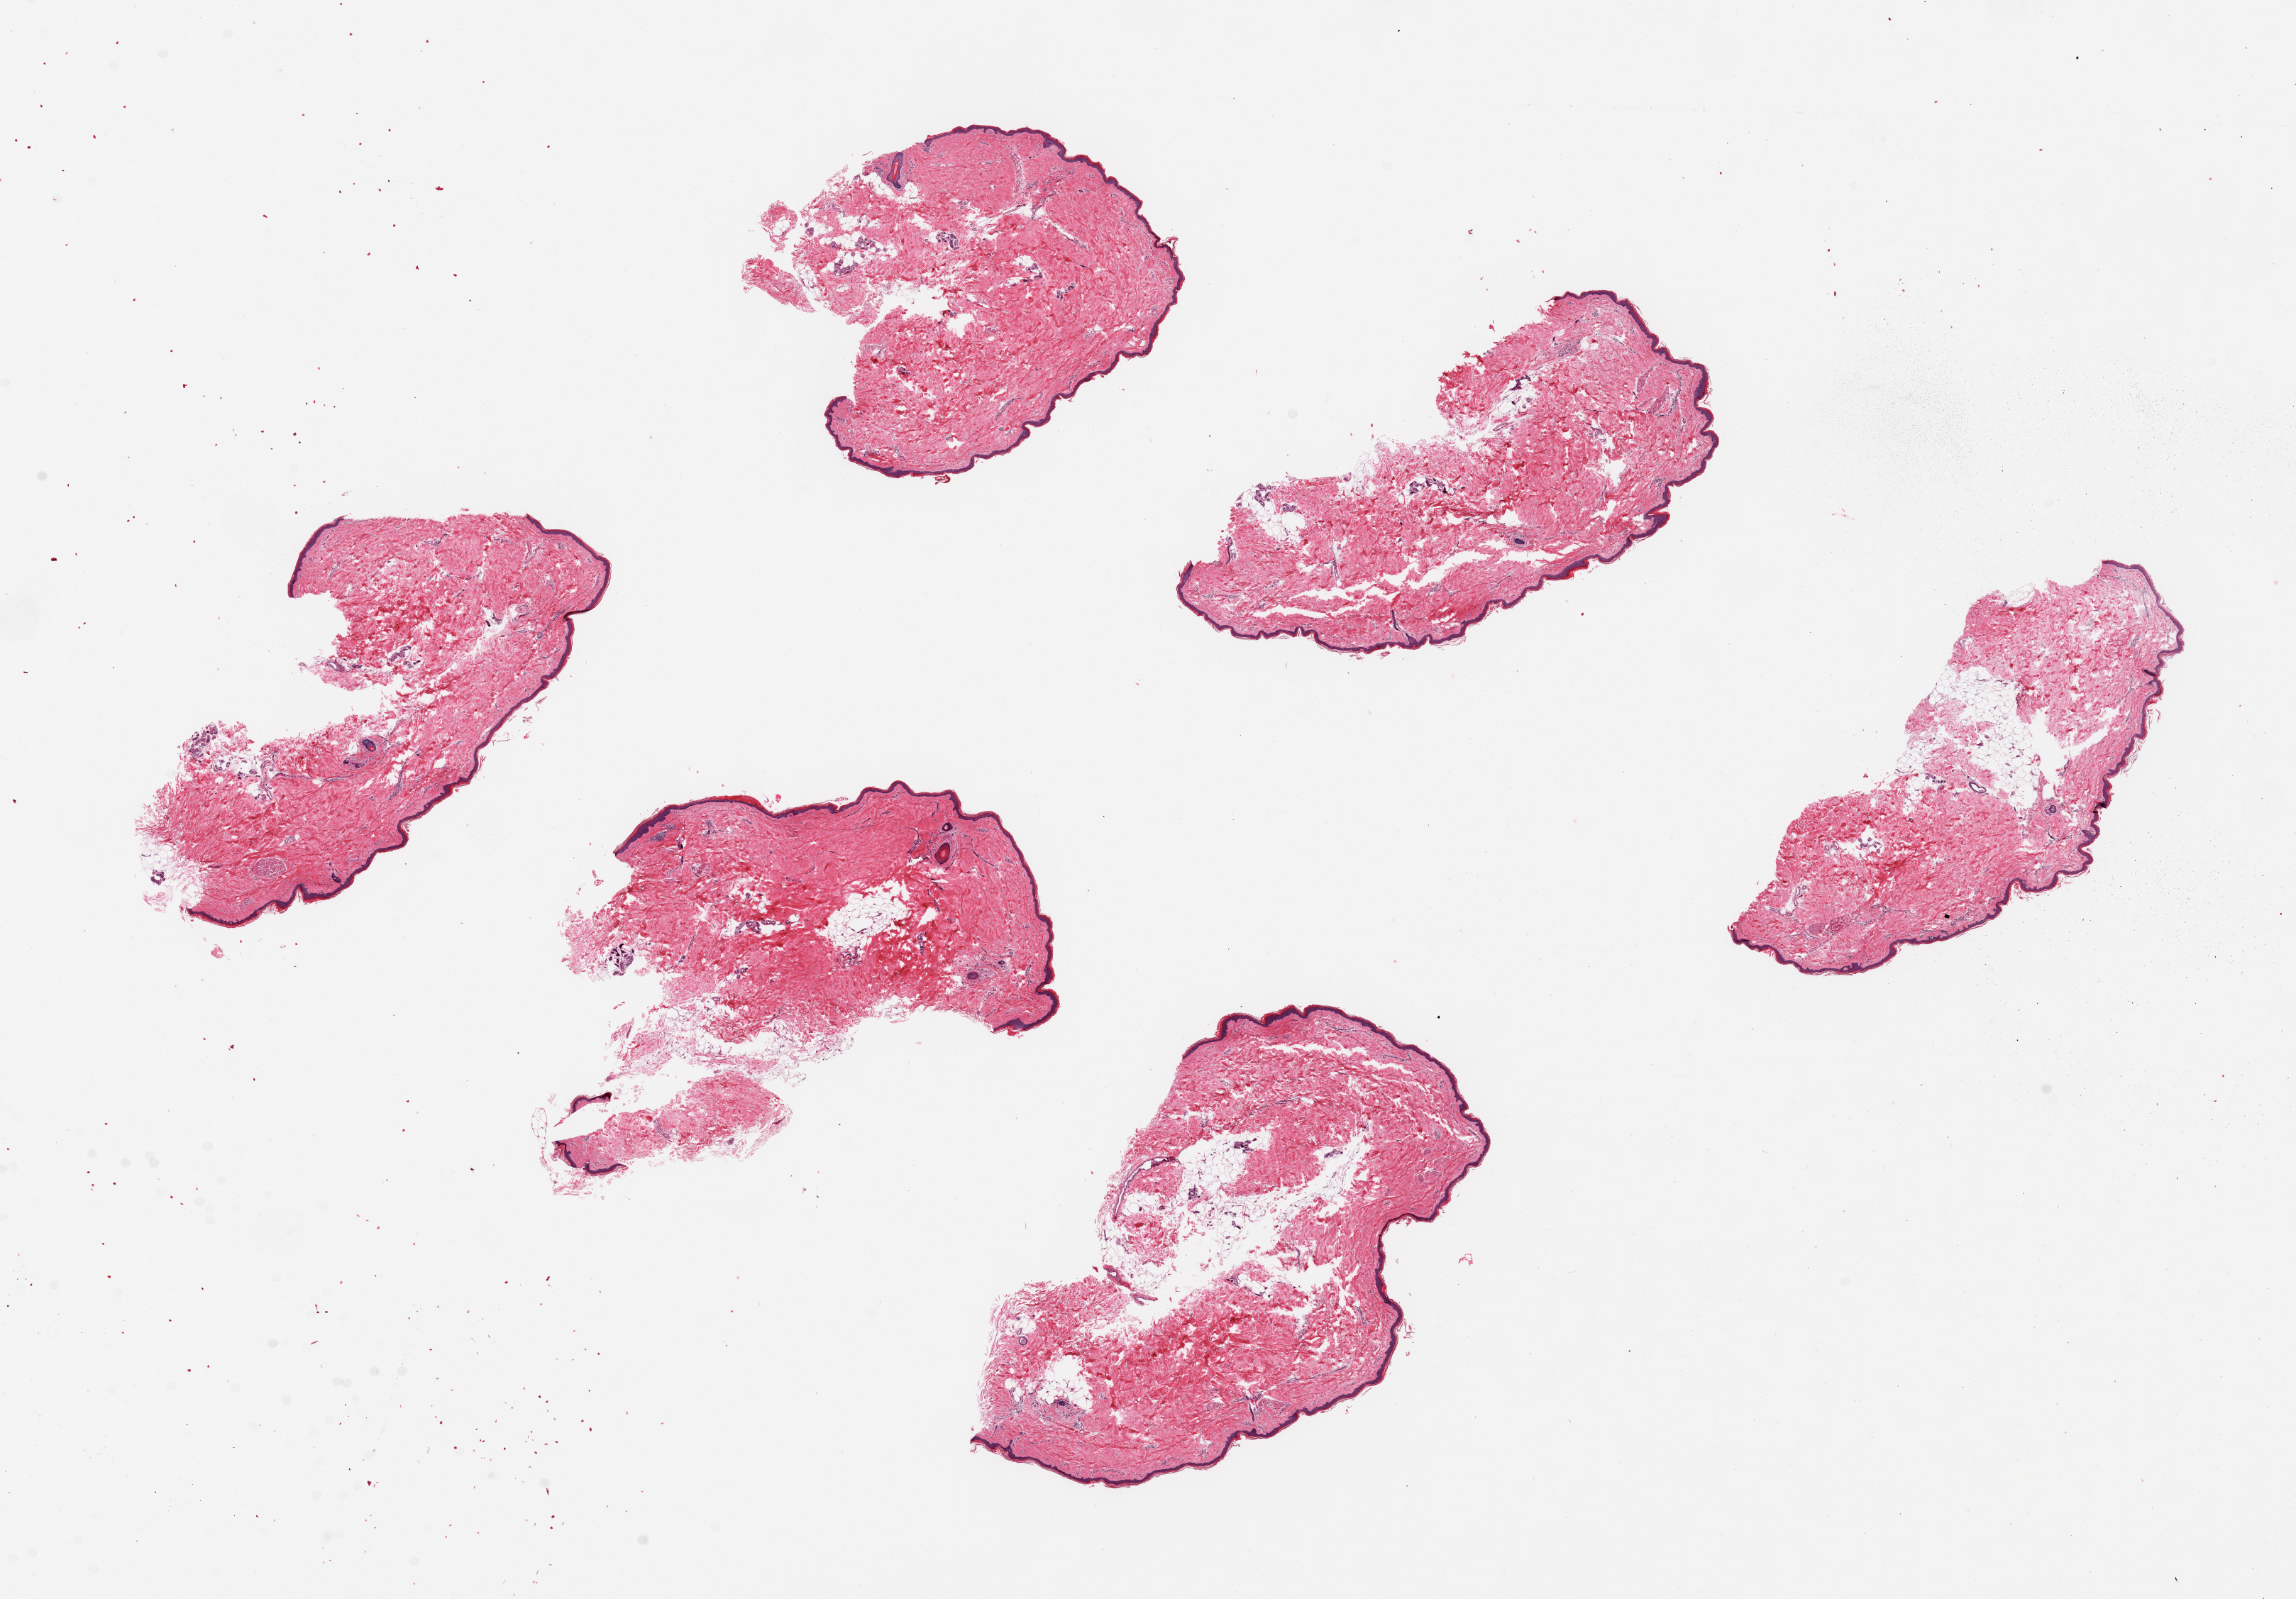
Digitized haematoxylin and eosin-stained section, shown as a low-resolution overview of the whole scanned area (about 25.6 x 17.8 mm); PAXgene-fixed paraffin-embedded (PFPE) section; sampled site (target tissue): skin of lower leg; tissue donor sample. Donor sex: female.
- pathologist's review note for this sample: 6 ~6x2.5mm pieces. Squamous epithelium is ~1.5-2% of thickness (~40-50 microns)